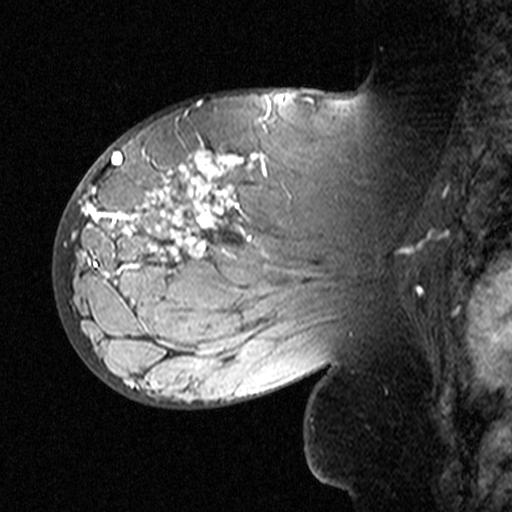
Breast MRI (dynamic contrast-enhanced), one sagittal slice; slice 26 of 44 in the series (ordered by position); dynamic contrast-enhanced study with each time point stored as its own series, time point 2 of 3 at this slice position (early post-contrast, ordered by acquisition time); 1.5 T; TE 4.5 ms, TR 11 ms; 3 mm slice thickness; 512 × 512 image matrix. Female patient, age 53 years. From the clinical record (not read from this slice): setting: breast cancer imaged before/during neoadjuvant chemotherapy; receptor status: HR-positive, HER2-negative.
Outlined on this slice (semi-automatic segmentation, software-assisted and operator-edited):
- analysis volume of interest (the breast-tissue region the enhancement analysis was run in; not a lesion): box from (x=76, y=140) to (x=311, y=353) px
- tumour enhancement mask (voxels above the 90 % enhancement threshold inside the analysis volume of interest): (x=94, y=148)–(x=266, y=308)